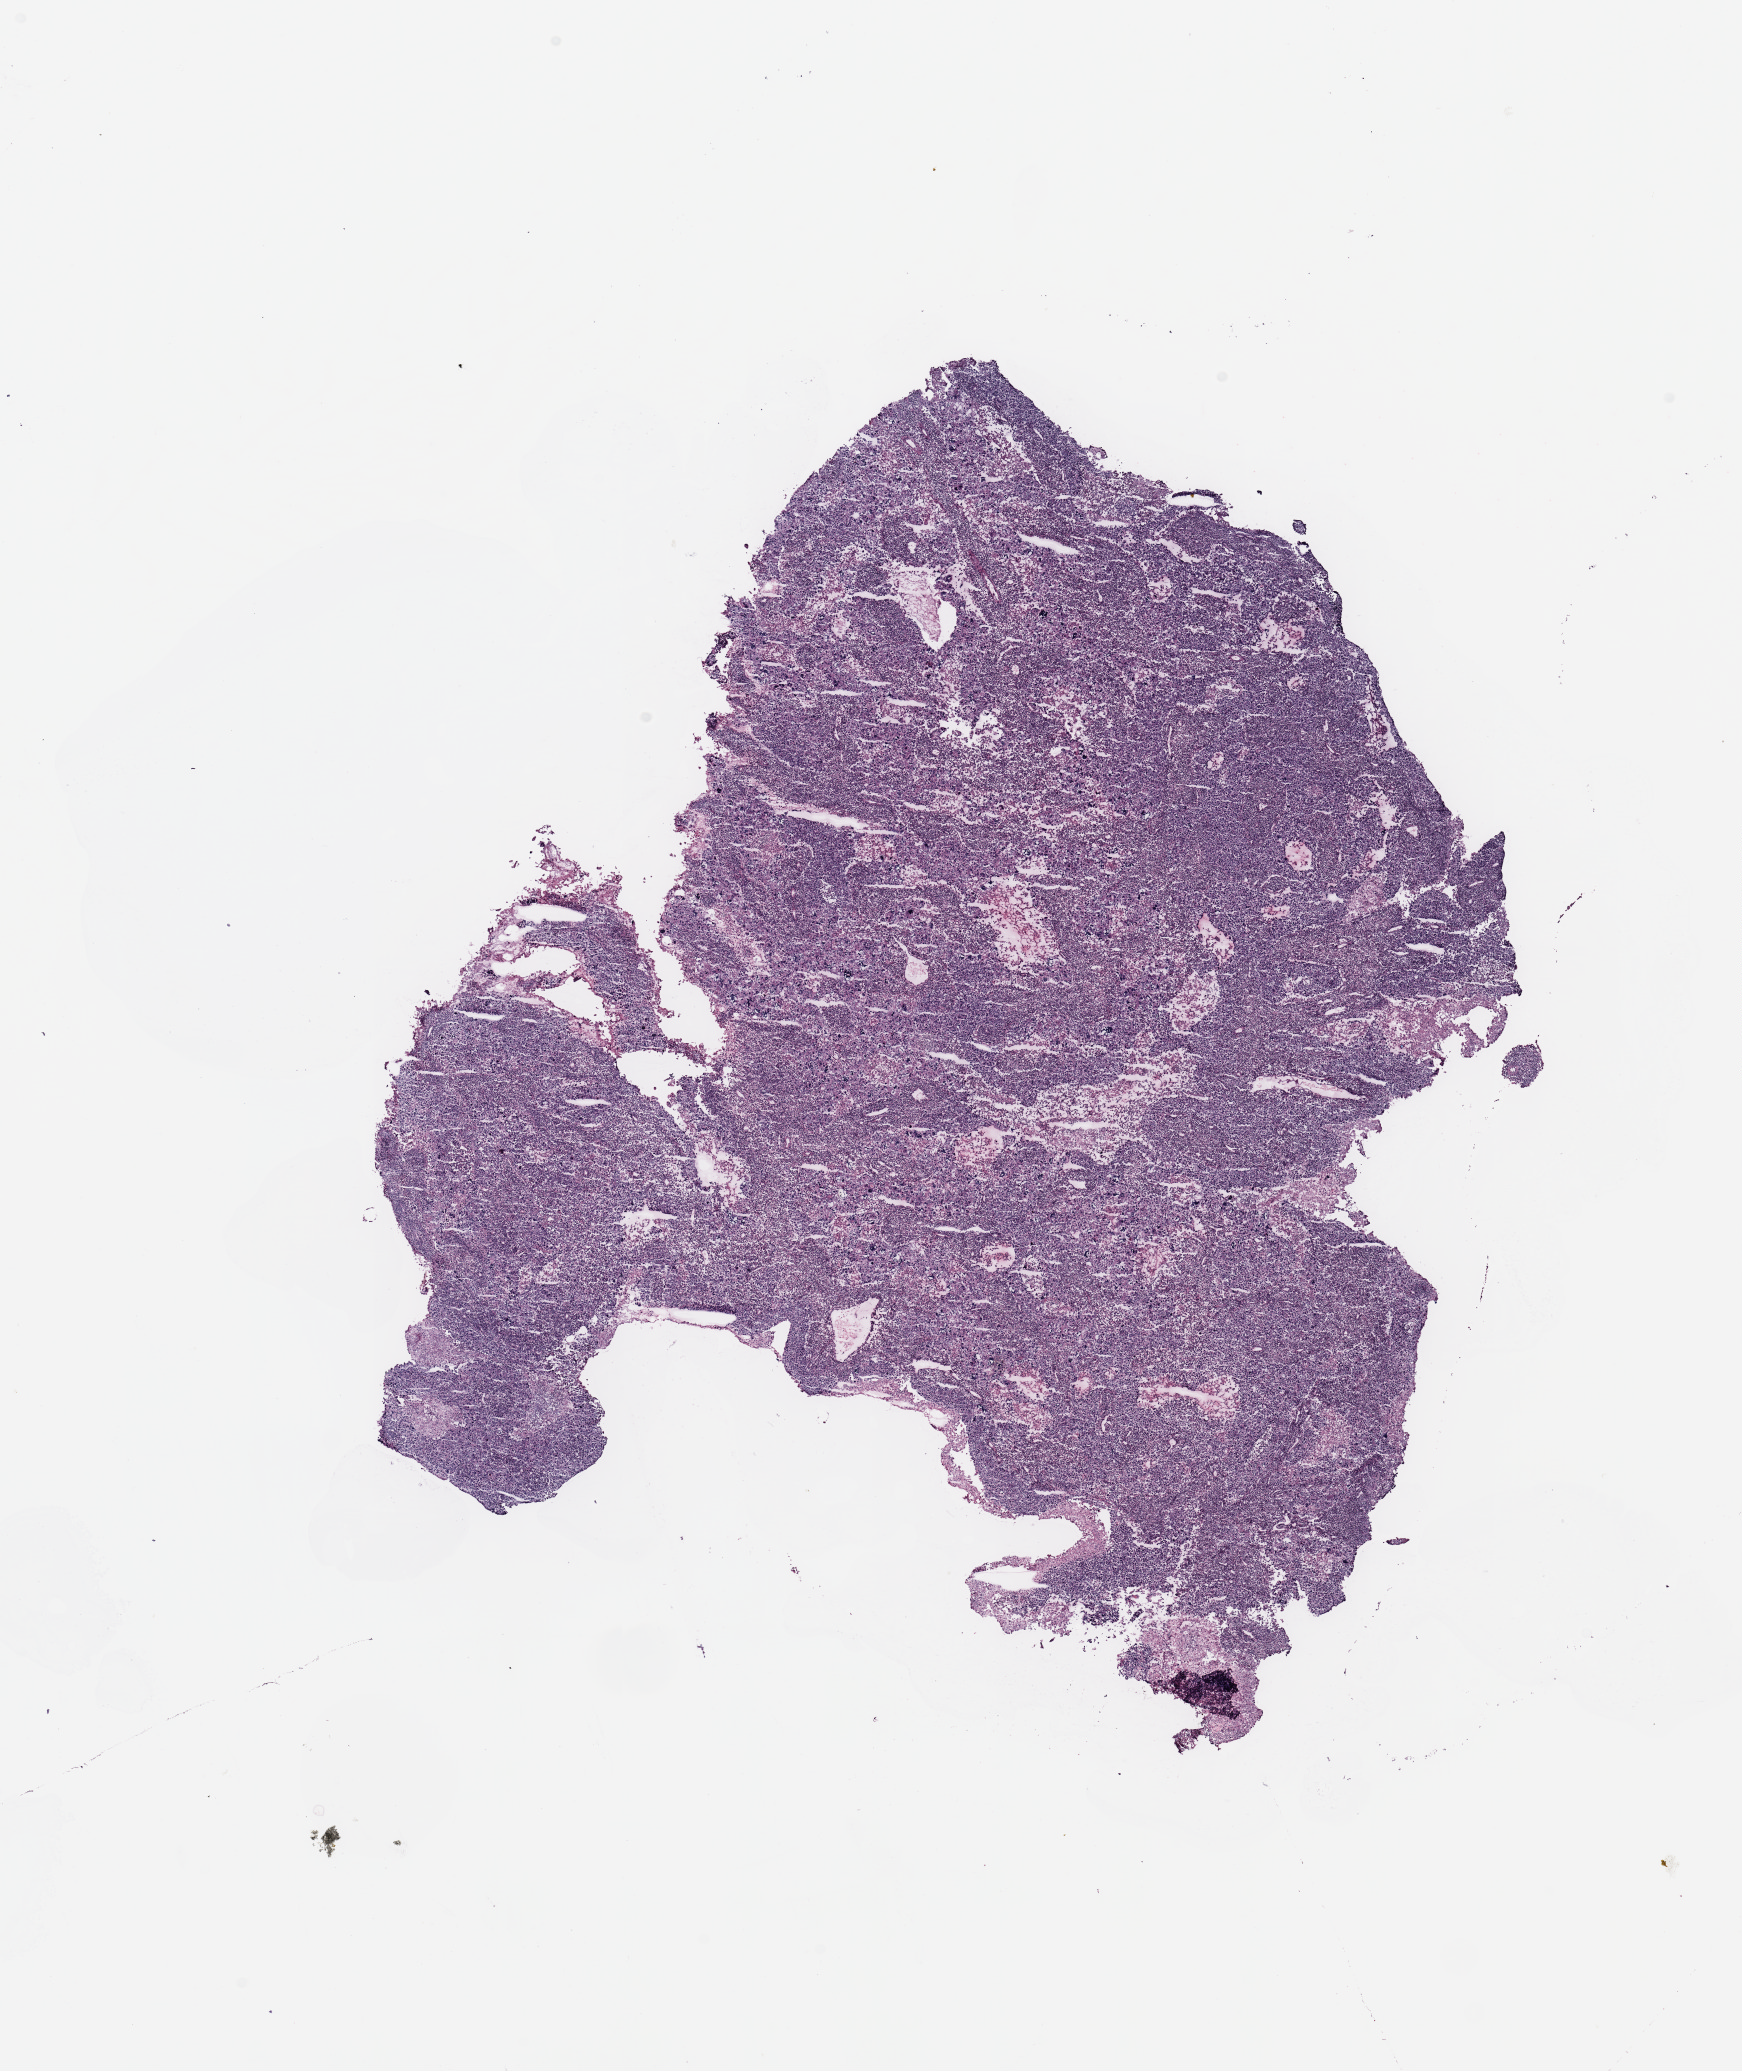
Hematoxylin and eosin (H&E) stained whole-slide image, low-resolution overview of the scanned area, about 13.8 x 16.4 mm (slide scanned at 20x). Breast, tissue type not recorded.
Patient diagnosis (cohort enrolment): breast cancer (breast).